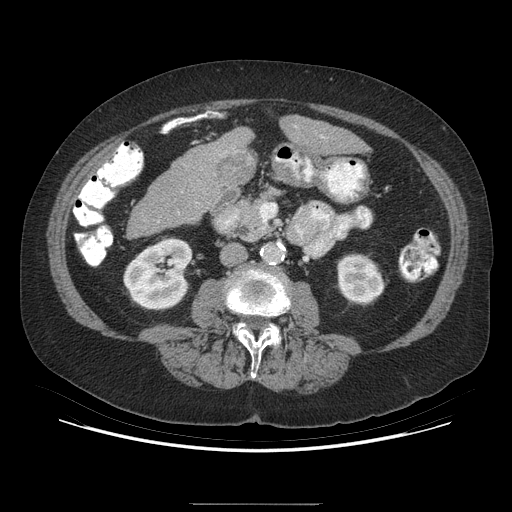
Contrast-enhanced abdominal CT (liver protocol), one axial slice; slice 129 of 192 in the series (ordered by position); 140 kVp; soft-tissue window (W 400 / L 40 HU); 2.5 mm slice thickness; 512 × 512 image matrix. From the clinical record (not read from this slice): diagnosis: hepatocellular carcinoma (patient treated with transarterial chemoembolisation; whether this scan precedes or follows treatment is not stated here); TNM stage (as recorded): Stage-I; Child-Pugh class: A; tumour differentiation: moderately differentiated; tumour nodularity: uninodular.
Annotated regions visible in this slice (semi-automatically segmented with operator editing):
- liver parenchyma outside the tumour (the mass and vessels are separate outlines, so this box may not span the whole liver): bounding box (x1, y1, x2, y2) in pixels: (280, 116, 359, 154)
- mass: (217, 150, 256, 189)